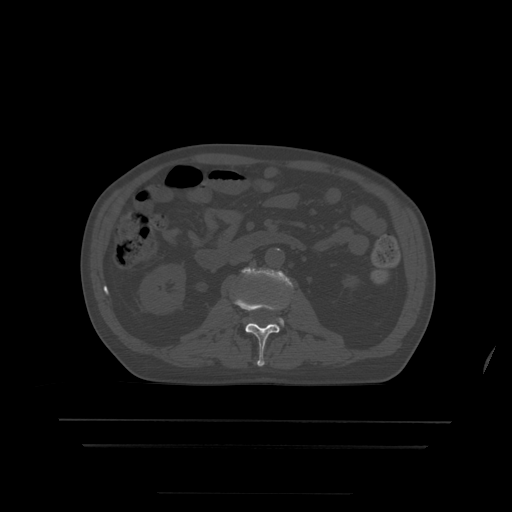
CT including the spine, one axial slice; slice 137 of 522 in the series (ordered by position); bone window (W 1800 / L 400 HU); 1.25 mm slice thickness; 512 × 512 image matrix, field of view 436 × 436 mm. Patient age 68 years. Case-level facts recorded for this patient, not image findings: primary cancer: urothelial.
Annotated regions visible in this slice (semi-automatically segmented with operator editing):
- L2 vertebra: box from (x=235, y=297) to (x=280, y=367) px
- L3 vertebra: (x=243, y=268)–(x=292, y=325)